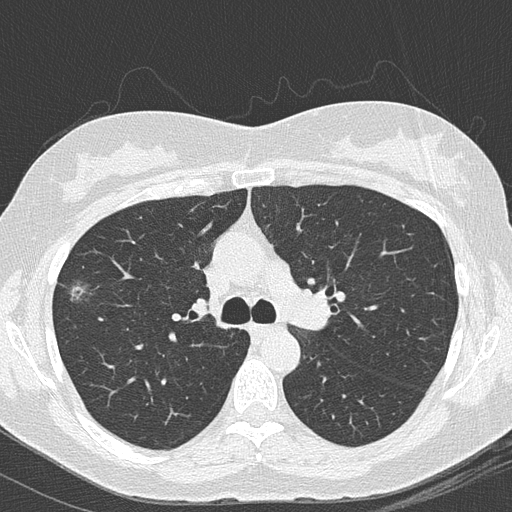
Axial slice from a low-dose chest CT screening exam. Second annual screen. Lung window (W 1500 / L -600 HU). 120 kVp. Slice 51 of 157 in the series. Female participant, aged 64 years at enrolment.
Lesion marked by an expert reader, bounding box (x1, y1, x2, y2) in pixels: (47, 262, 107, 315). Screening reader's record for this exam (one nodule recorded; not confirmed to be the boxed lesion): non-calcified nodule or mass ≥4 mm, right upper lobe, 16 × 13 mm, mixed attenuation, pre-existing on the prior screen: yes; interval growth: yes. Official screen result: positive, other. Participant outcome: lung cancer diagnosed 112 days after this screen — bronchiolo-alveolar adenocarcinoma, NOS, right upper lobe, well differentiated (G1), stage IA (AJCC 6th edition), 10 mm at pathology.